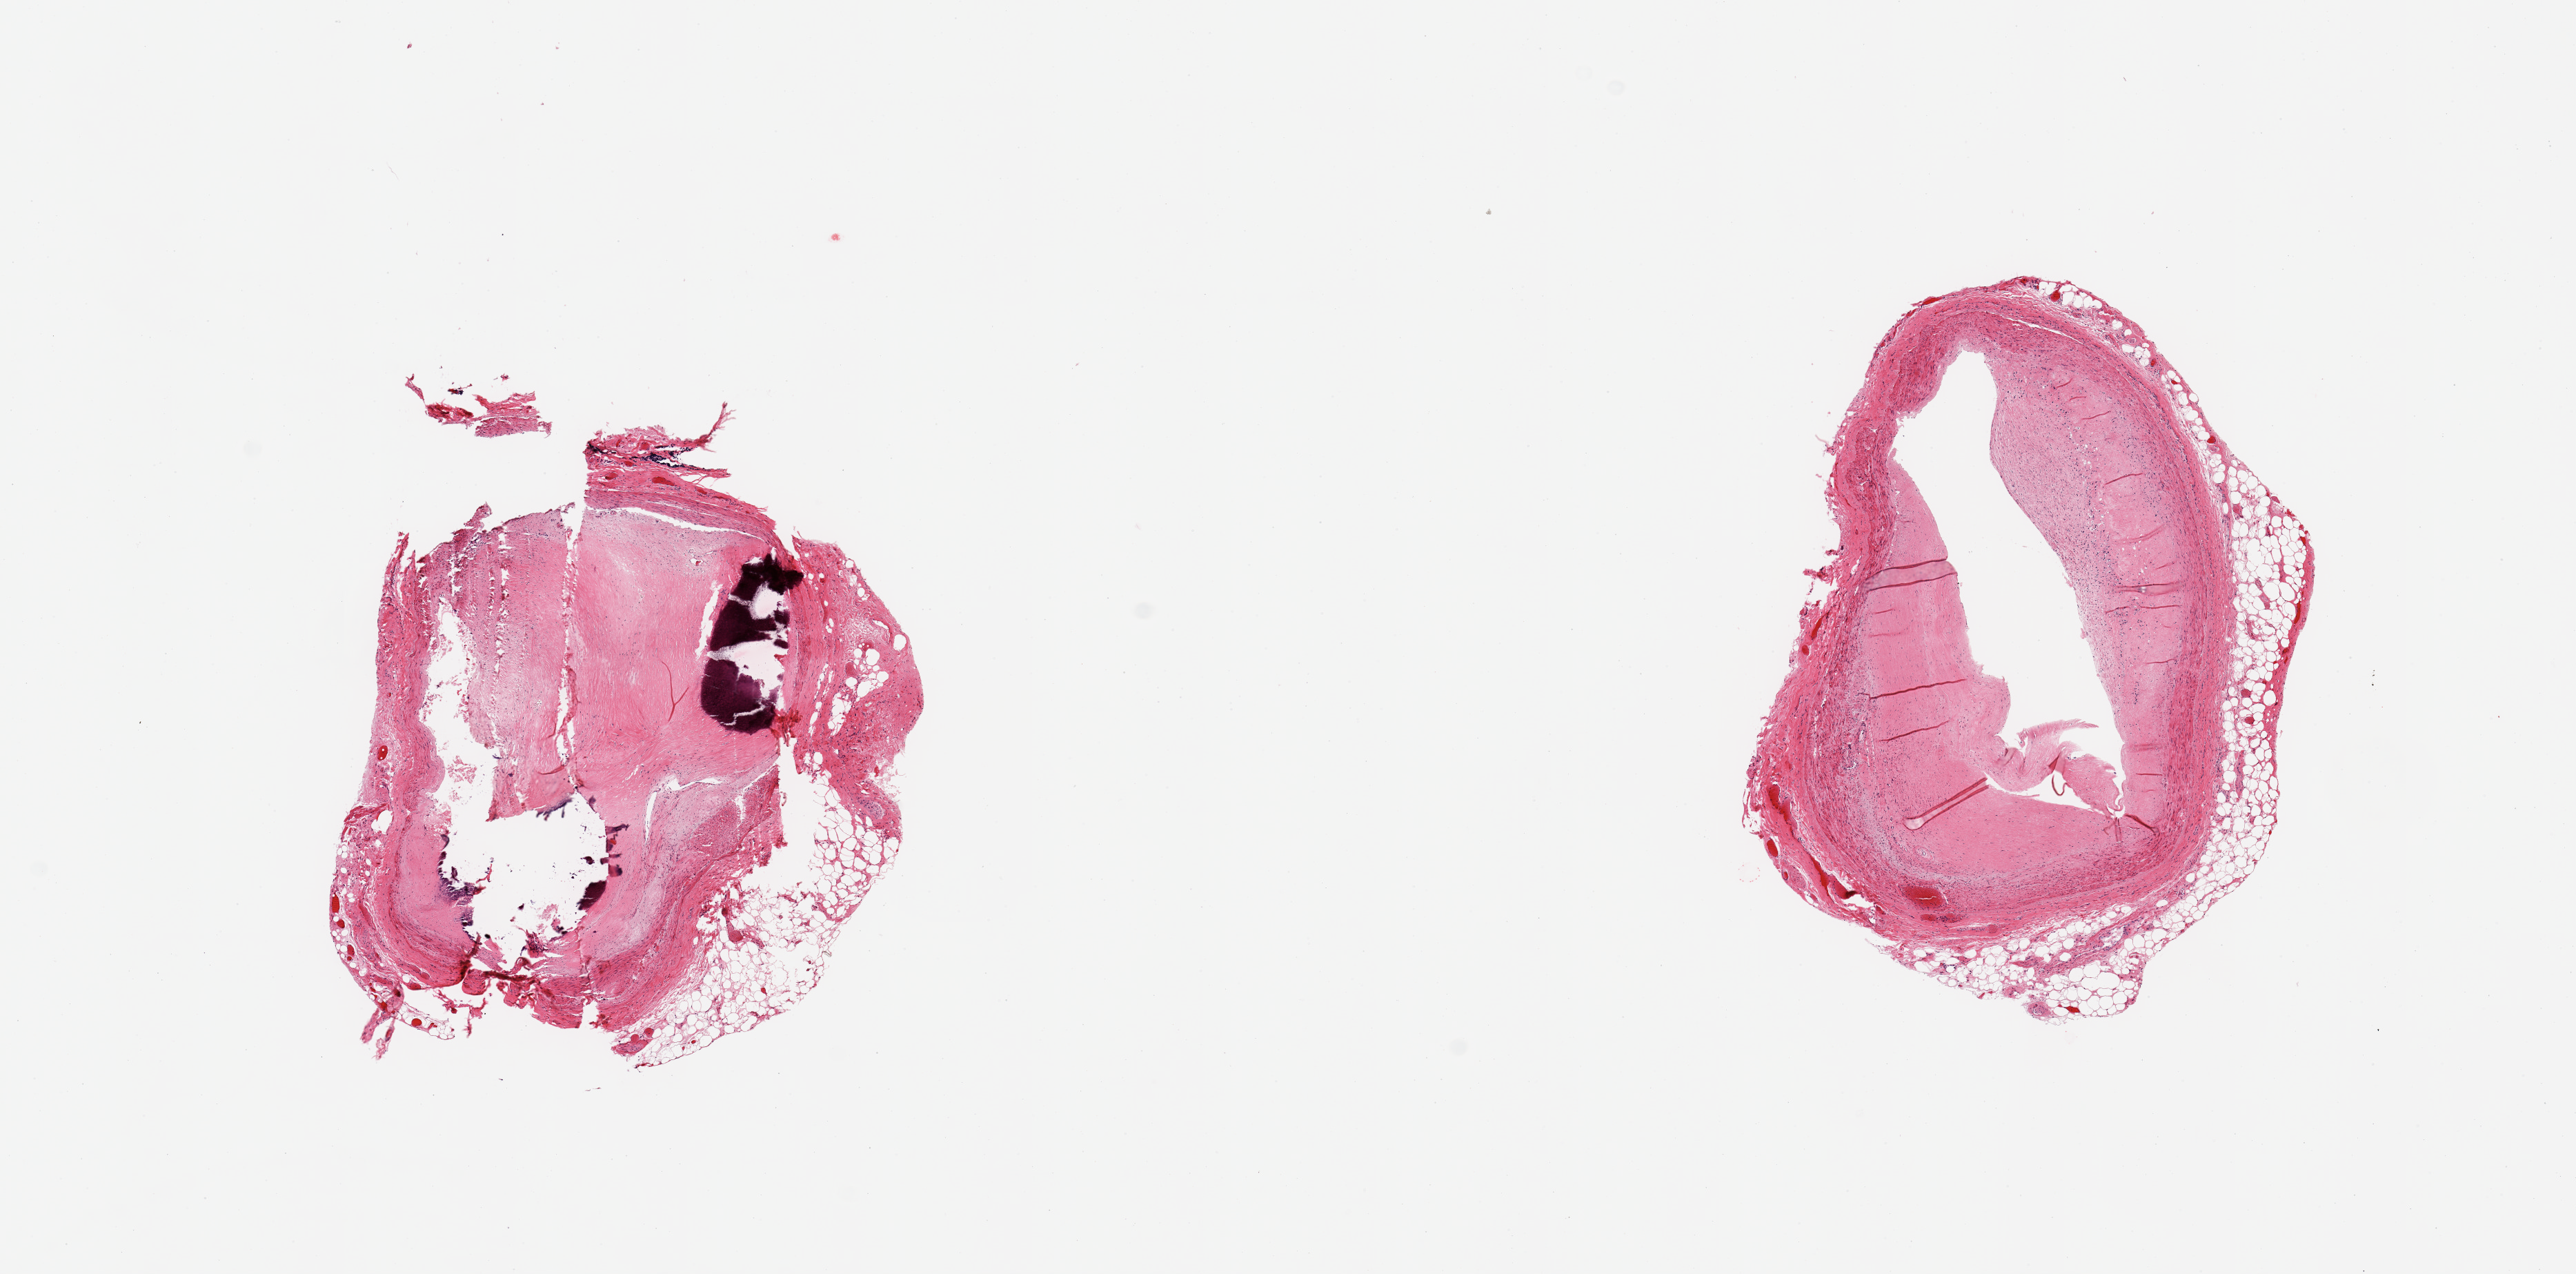
Hematoxylin and eosin (H&E) whole-slide image, shown as a low-resolution overview of the whole scanned area (about 14.8 x 7.3 mm), PAXgene-fixed paraffin-embedded (PFPE) section, sampled site (target tissue): coronary artery, donor tissue sample.
Review note (as recorded): 2 pieces; severe calcific atherosclerosis with narrowing of the lumen, partial rim of attached fat (15-20%).